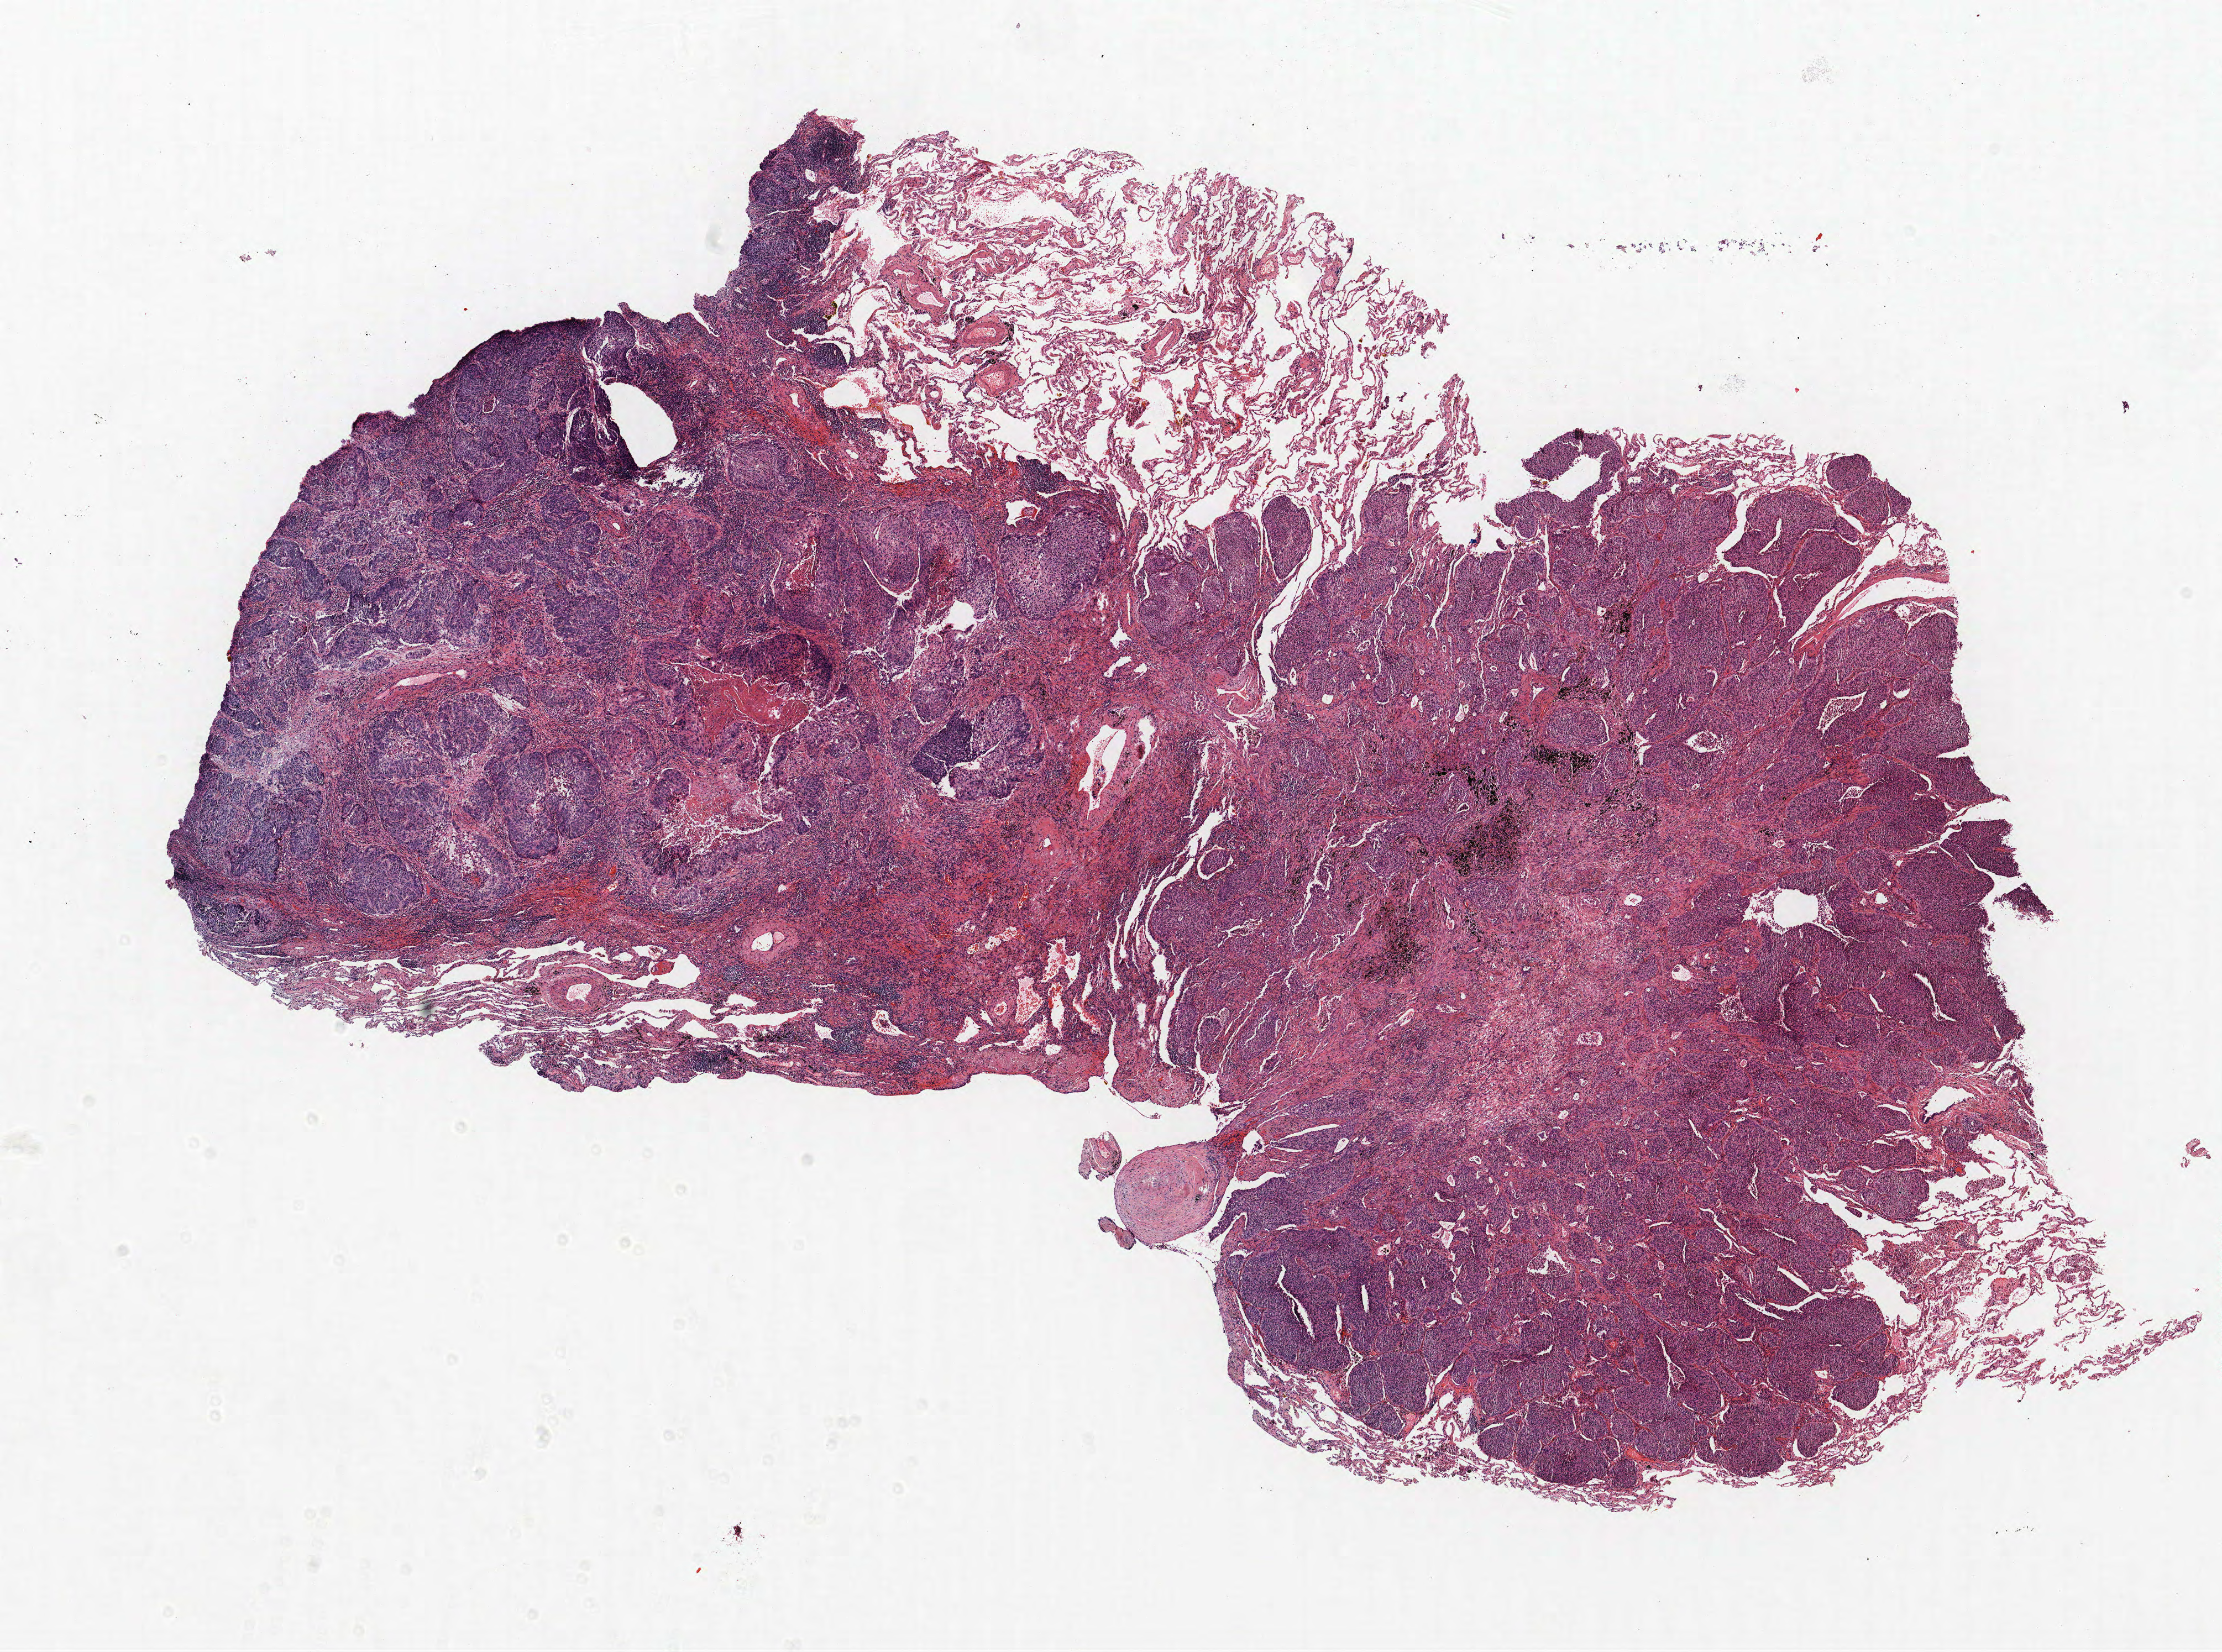
Whole-slide histology image, H&E — whole scanned area (about 16.1 x 12.0 mm, slide scanned at 40x) shown as a low-resolution overview, FFPE section, lung. Female, age 70 at enrolment. Former smoker at enrolment. Grade: moderately differentiated (G2).
Stage (AJCC 6th edition): IA. Primary tumour location (clinical record): right lower lobe. Tumour size (pathology): 16 mm. Participant's lung-cancer diagnosis: Squamous cell carcinoma, NOS.